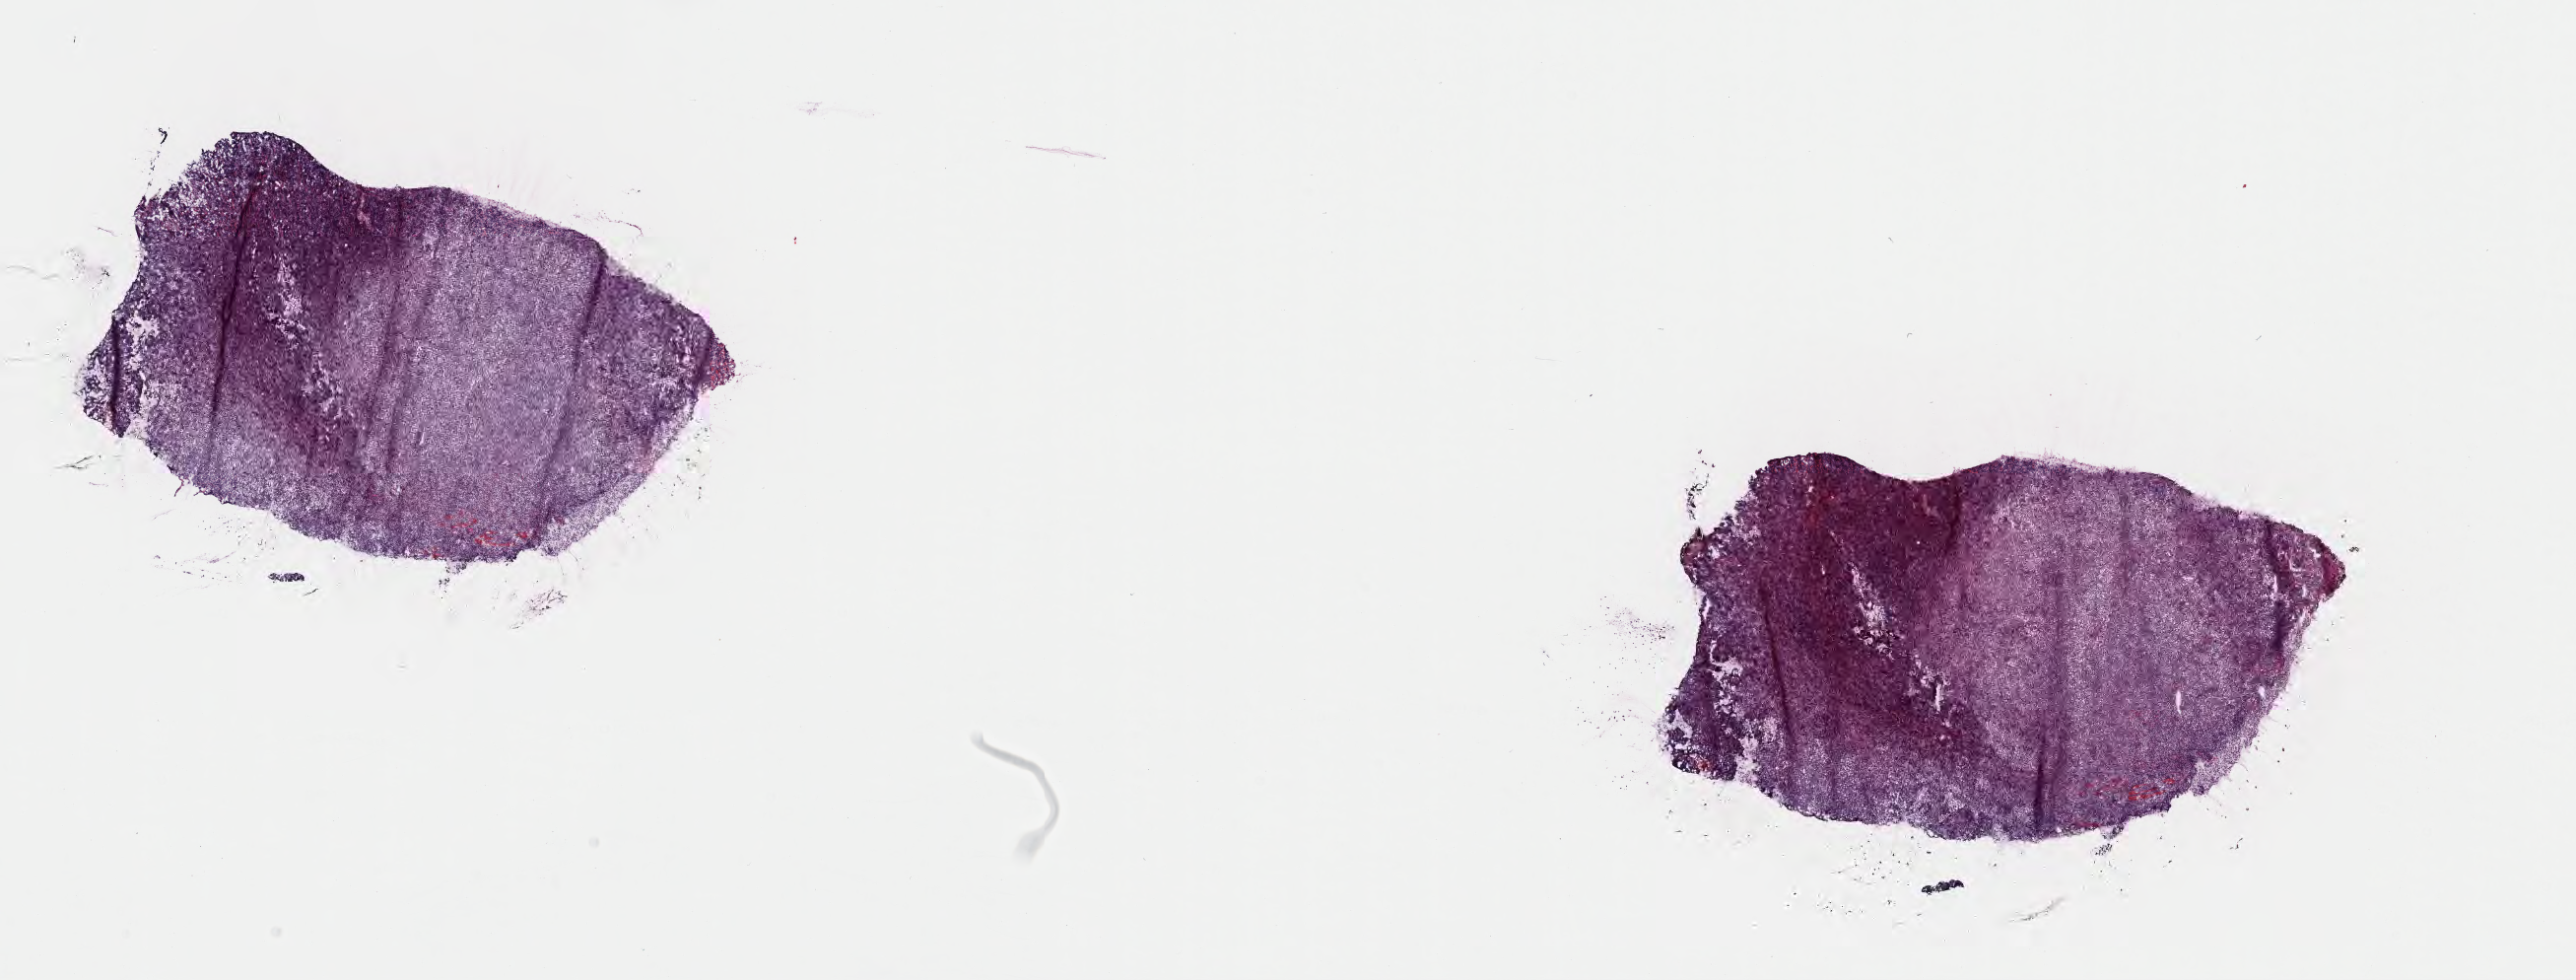
Digitized haematoxylin and eosin-stained section — whole scanned area (about 21.1 x 8.0 mm) shown as a low-resolution overview. Cryosection. Specimen: primary tumor. Anatomic site: cranium. Patient female; aged 10. Composition of this section per pathologist review: tumor cells 85%, tumor nuclei 90%, stromal cells 5%, necrosis 10%, normal cells 0%. Infiltration values recorded for this section: lymphocyte infiltration 30%, monocyte infiltration 35%, neutrophil infiltration 5%.
Section: bottom of the tissue portion. Histologic diagnosis: Diffuse large B-cell lymphoma, NOS. Ann Arbor stage (patient): Stage IV.